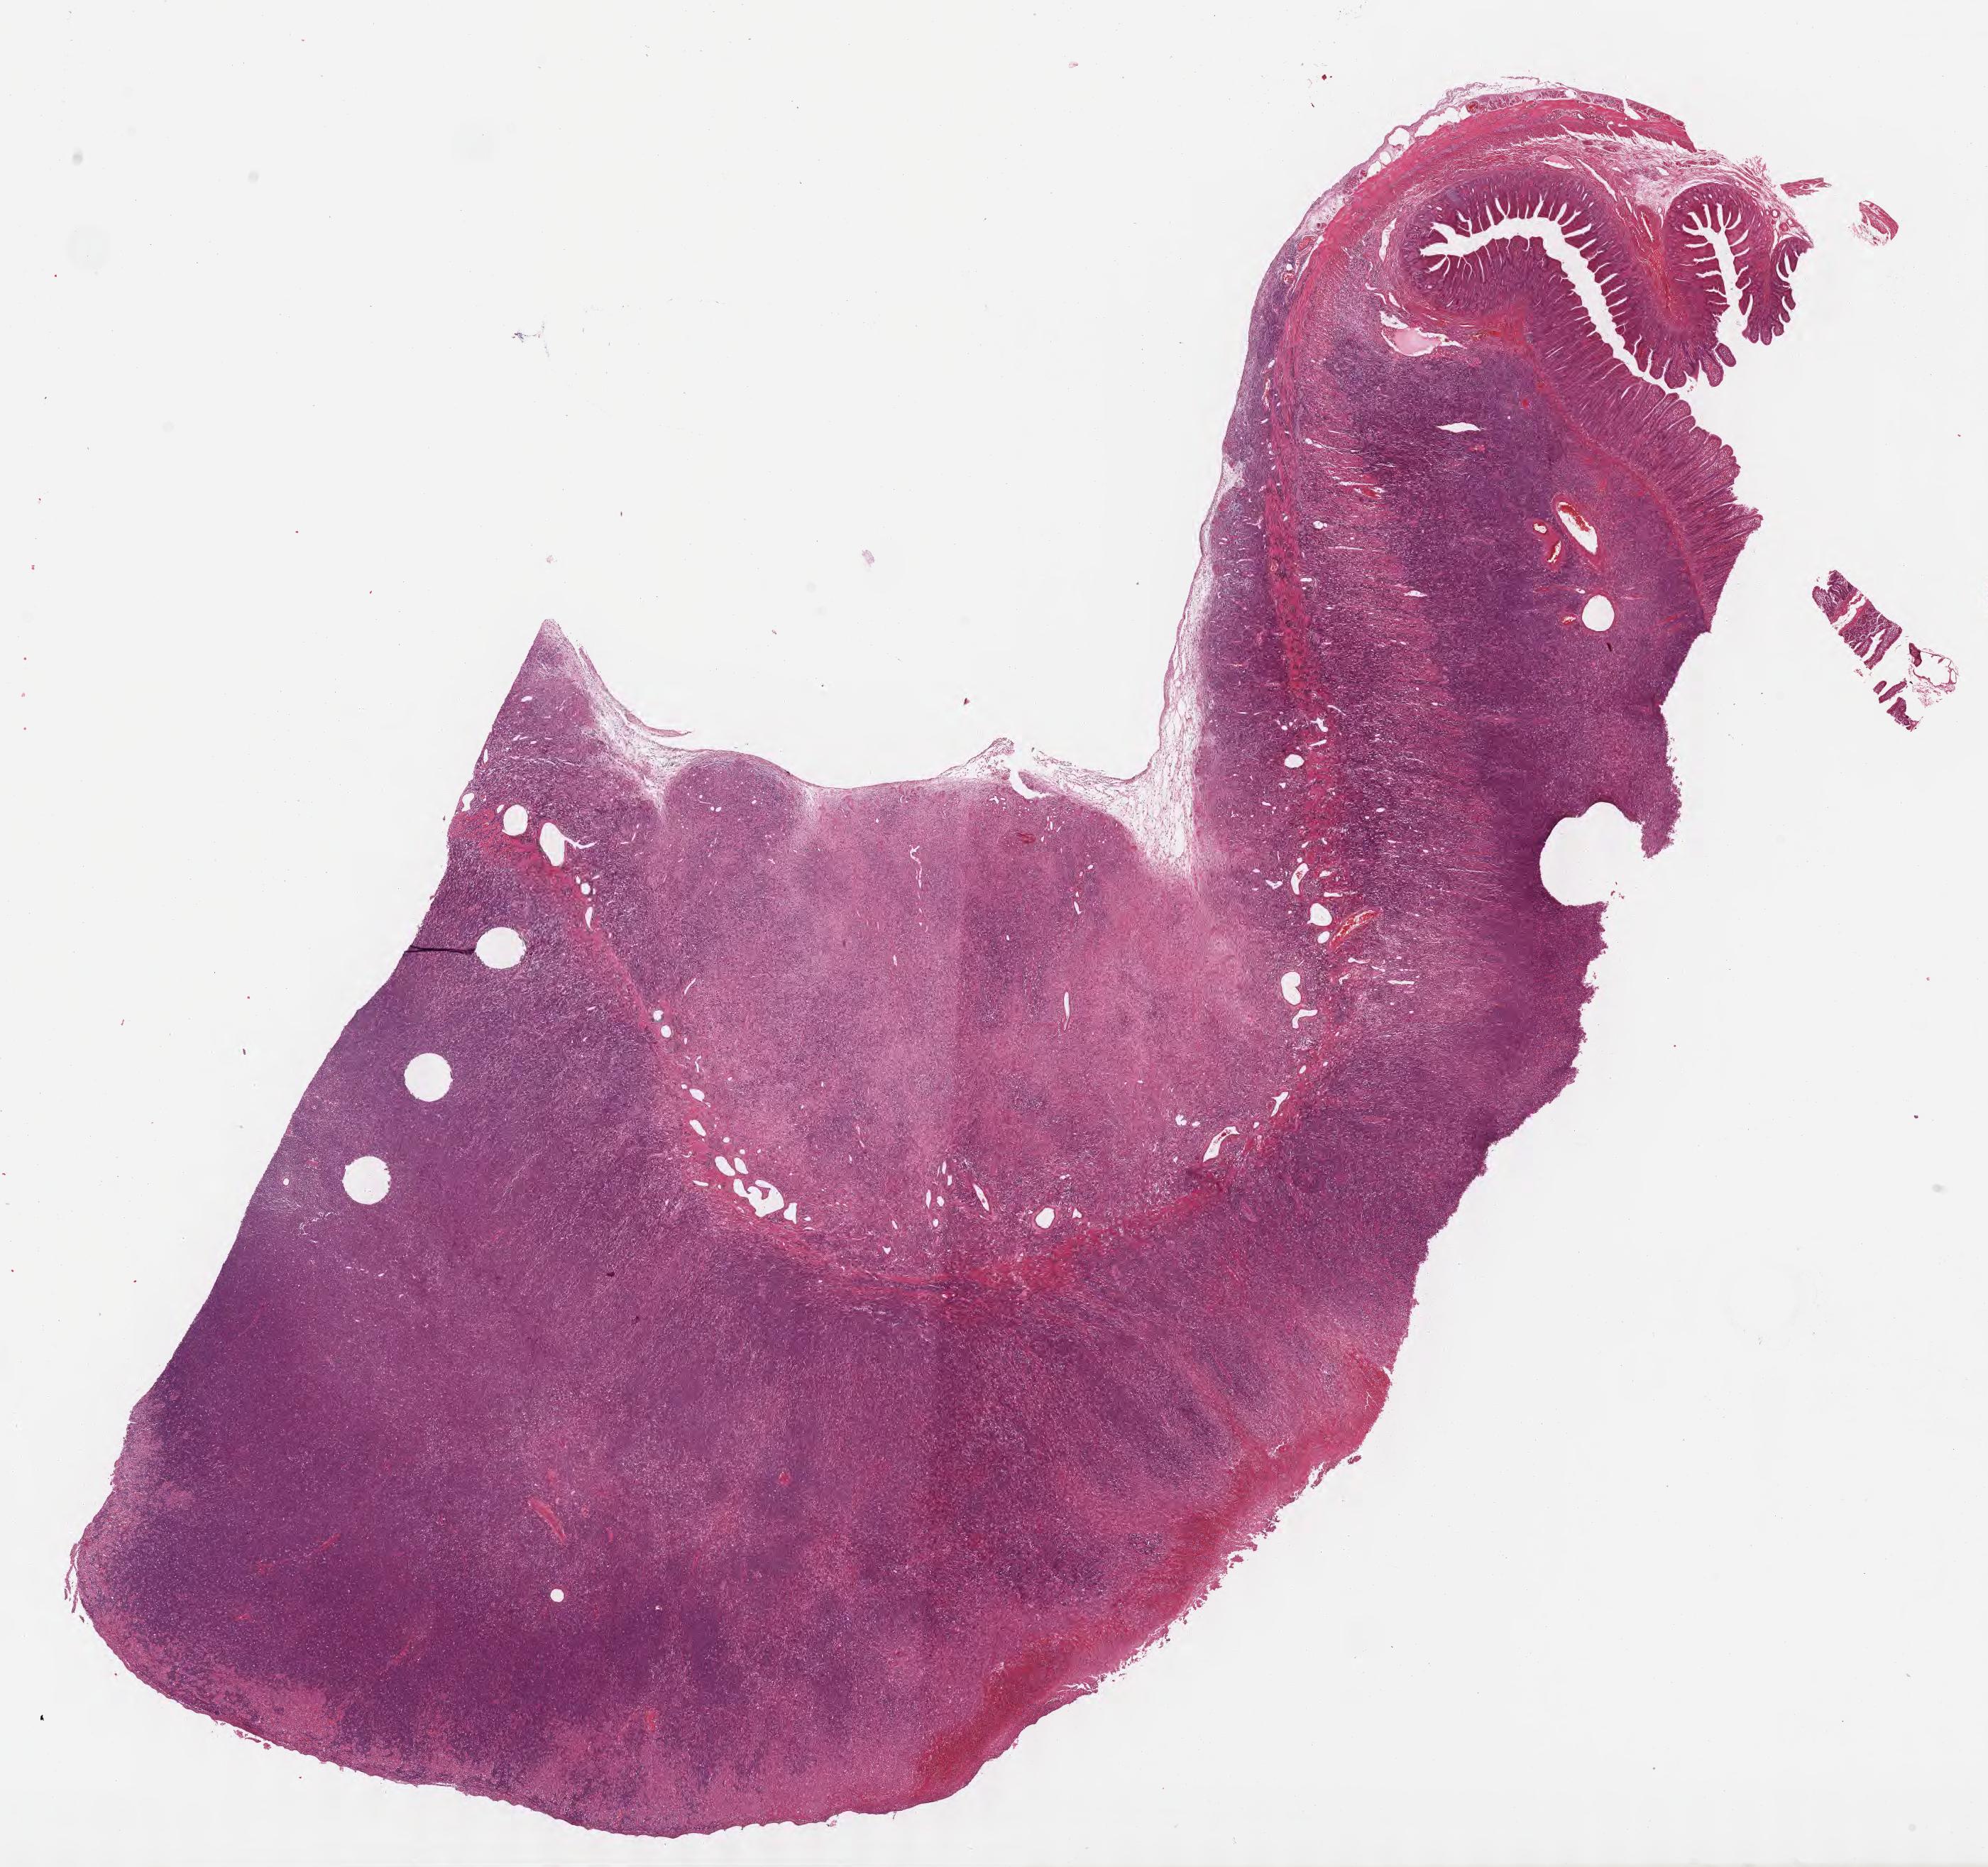
Whole-slide image, haematoxylin and eosin stain, low-resolution overview of the scanned area, about 22.6 x 21.3 mm. Formalin-fixed, paraffin-embedded (FFPE) tissue. Primary tumor. Male, age 4 years at initial diagnosis. Pathologist review of this section (percent, as recorded): tumor cells 75%, tumor nuclei 80%, stromal cells 10%, necrosis 5%, normal cells 10%. Infiltration values recorded for this section: lymphocyte infiltration 75%, monocyte infiltration 10%, neutrophil infiltration 5%.
- diagnosis: Burkitt lymphoma, NOS
- section: bottom of the tissue portion
- Ann Arbor stage (patient): Stage IV